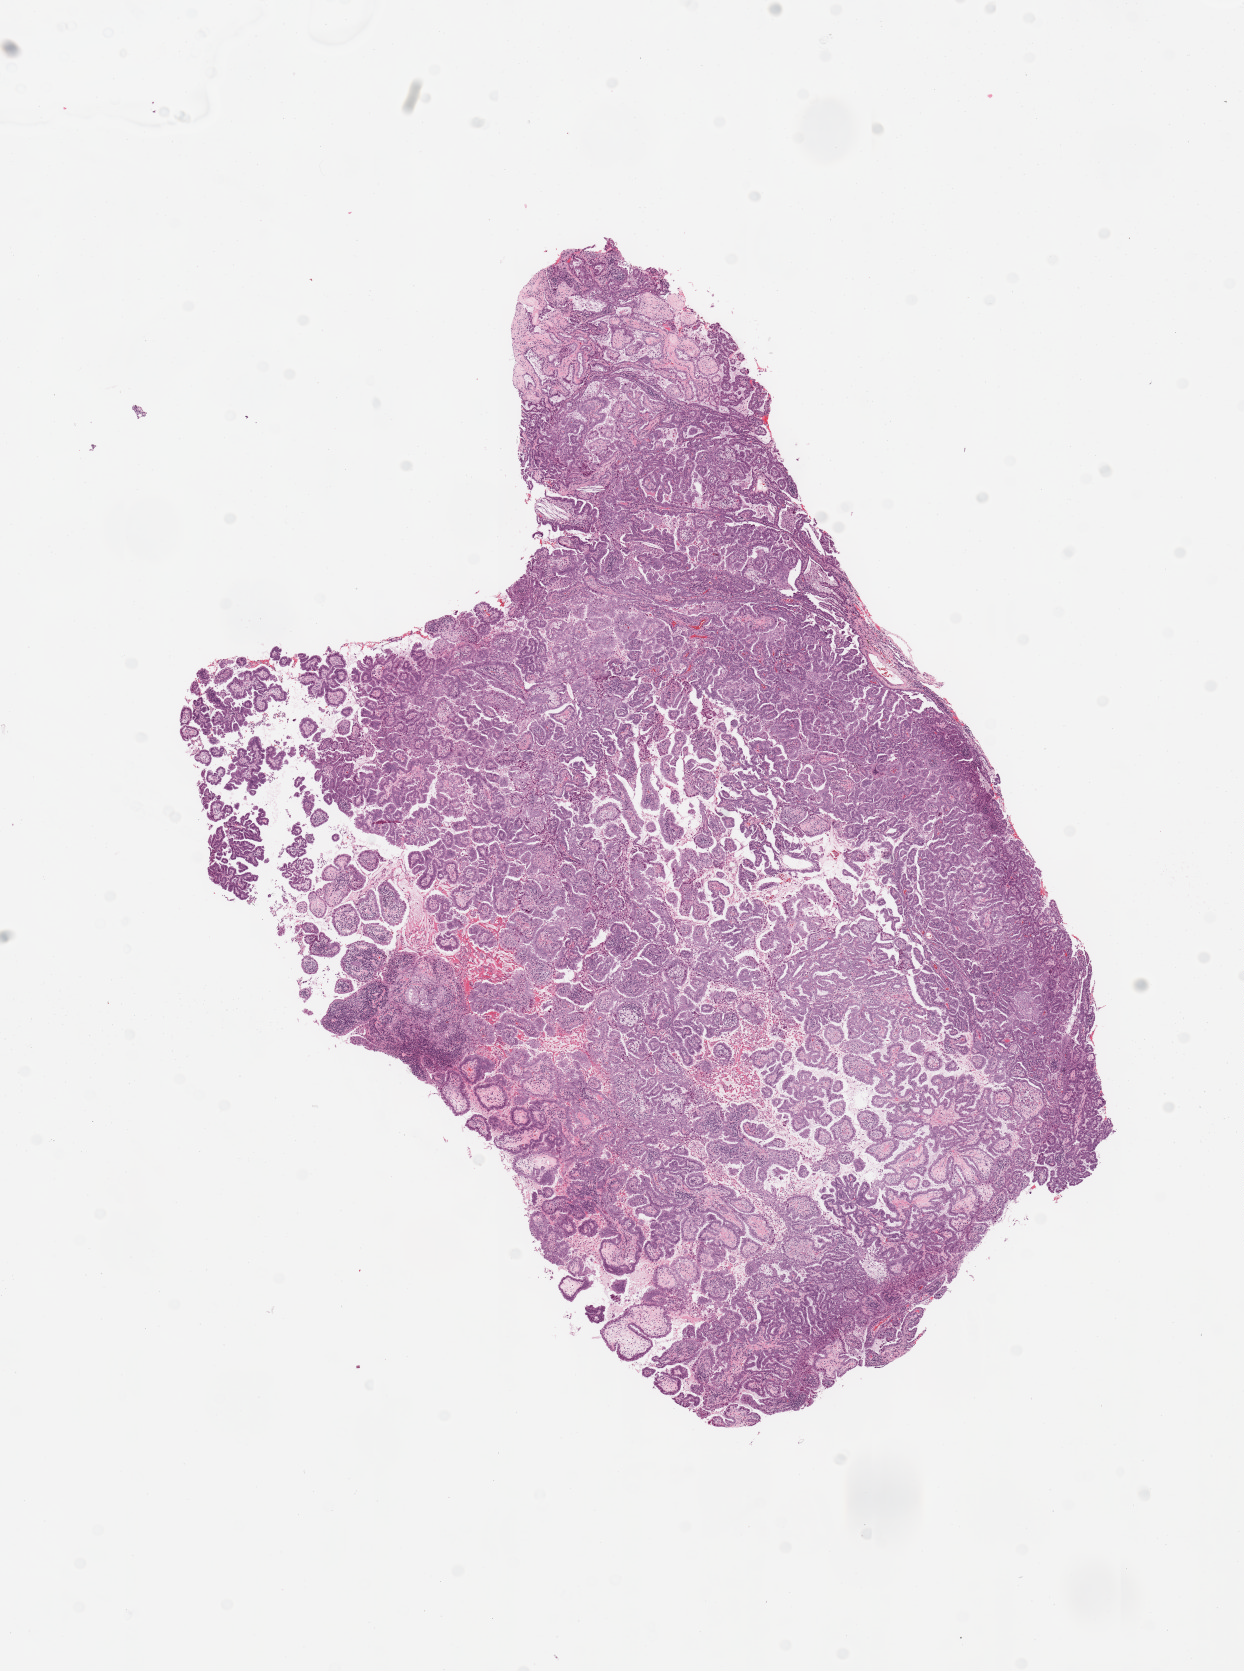
Whole-slide histology image, Hematoxylin and eosin (H&E) stained — whole scanned area (about 9.8 x 13.2 mm, acquisition: 20x scan) shown as a low-resolution overview, tumour tissue sample, sampled site: lung. Patient: male, age 70 years. Histologic grade: G1 (well differentiated). Slide review estimates, as recorded: tumour nuclei 80%, necrosis 5%.
- histologic diagnosis: Adenocarcinoma, NOS
- AJCC pathologic stage: IA
- primary tumour site (as recorded): right upper lobe